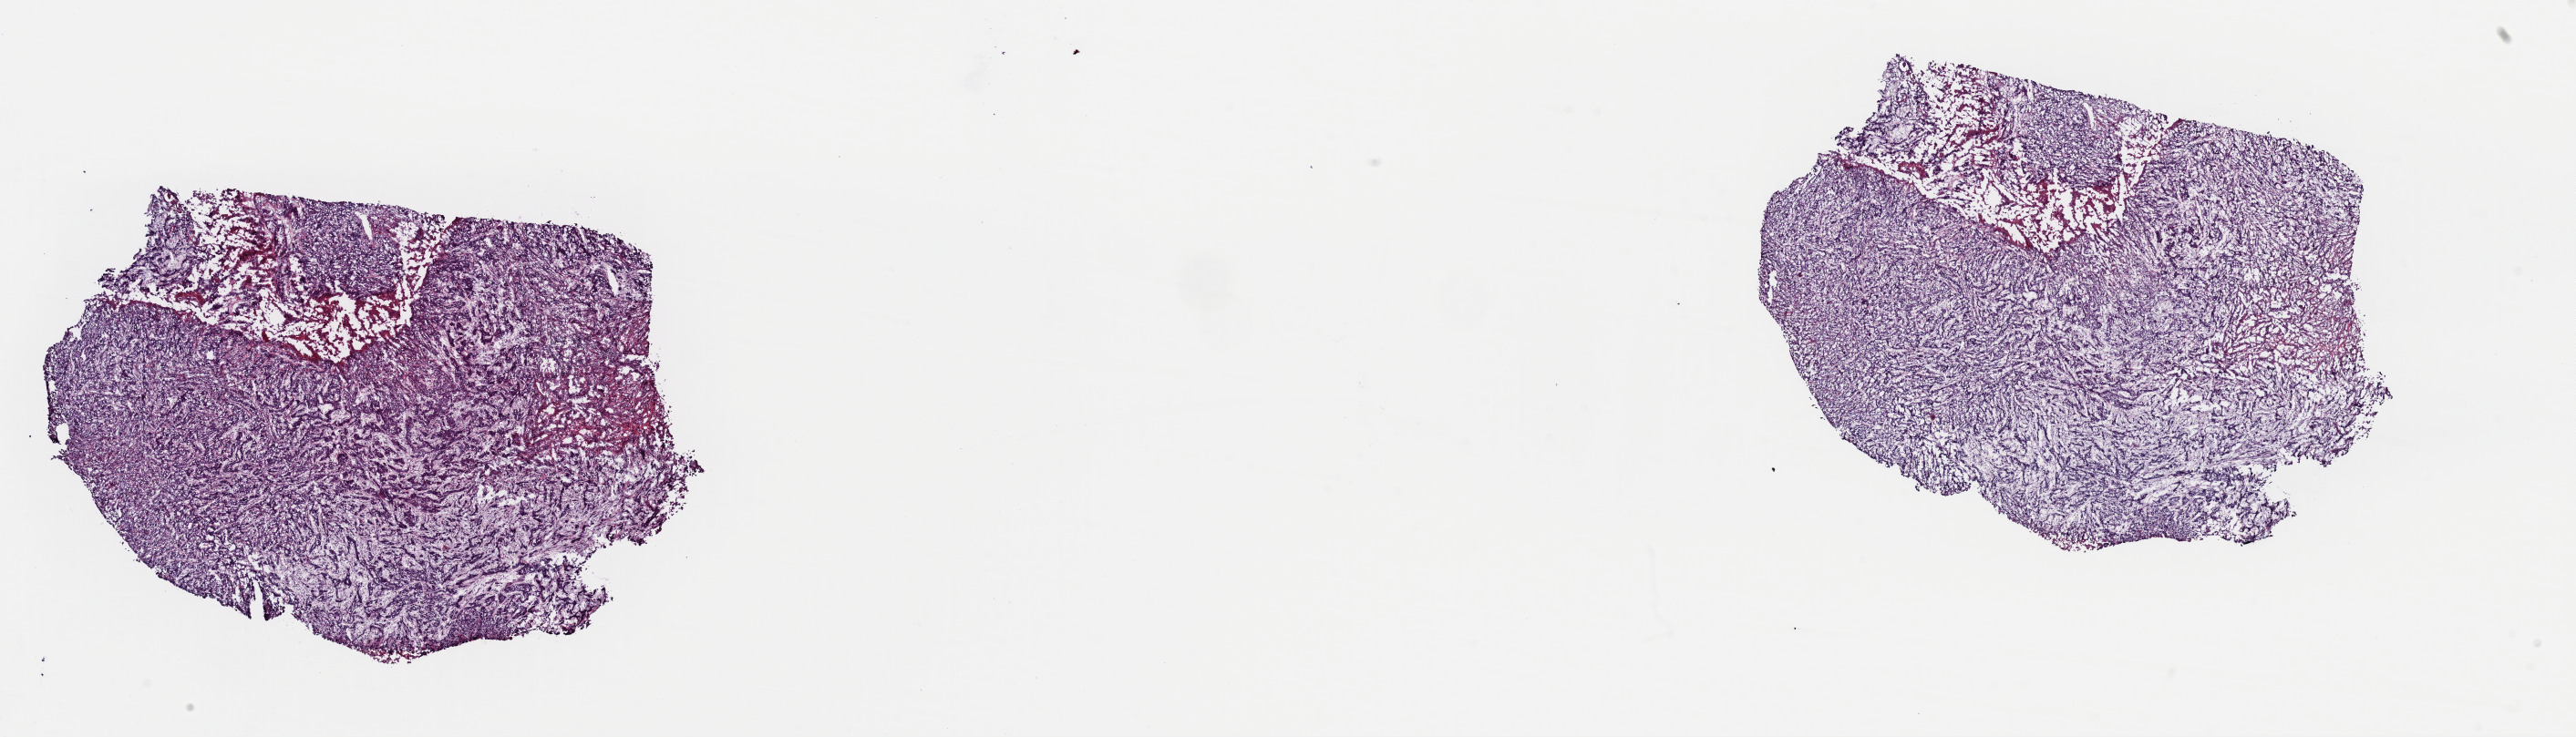
Digitized Hematoxylin and eosin (H&E) stained tissue section (whole slide) — a low-resolution overview of the entire scanned area, about 22.3 x 6.4 mm; frozen section from the top of the tissue portion; sample: primary tumour, head and neck. Male patient; age at initial diagnosis 64 years. Histologic grade: G3 (poorly differentiated). Pathologist review of this section (percent, as recorded): tumour cells 80%, tumour nuclei 90%, normal cells 0%, stromal cells 10%, necrosis 10%. Infiltration values recorded for this section: lymphocyte infiltration 0%, monocyte infiltration 0%, neutrophil infiltration 0%.
* laterality: left
* diagnosis: Squamous cell carcinoma, NOS (hypopharynx, NOS)
* AJCC pathologic stage: IVA (7th edition)